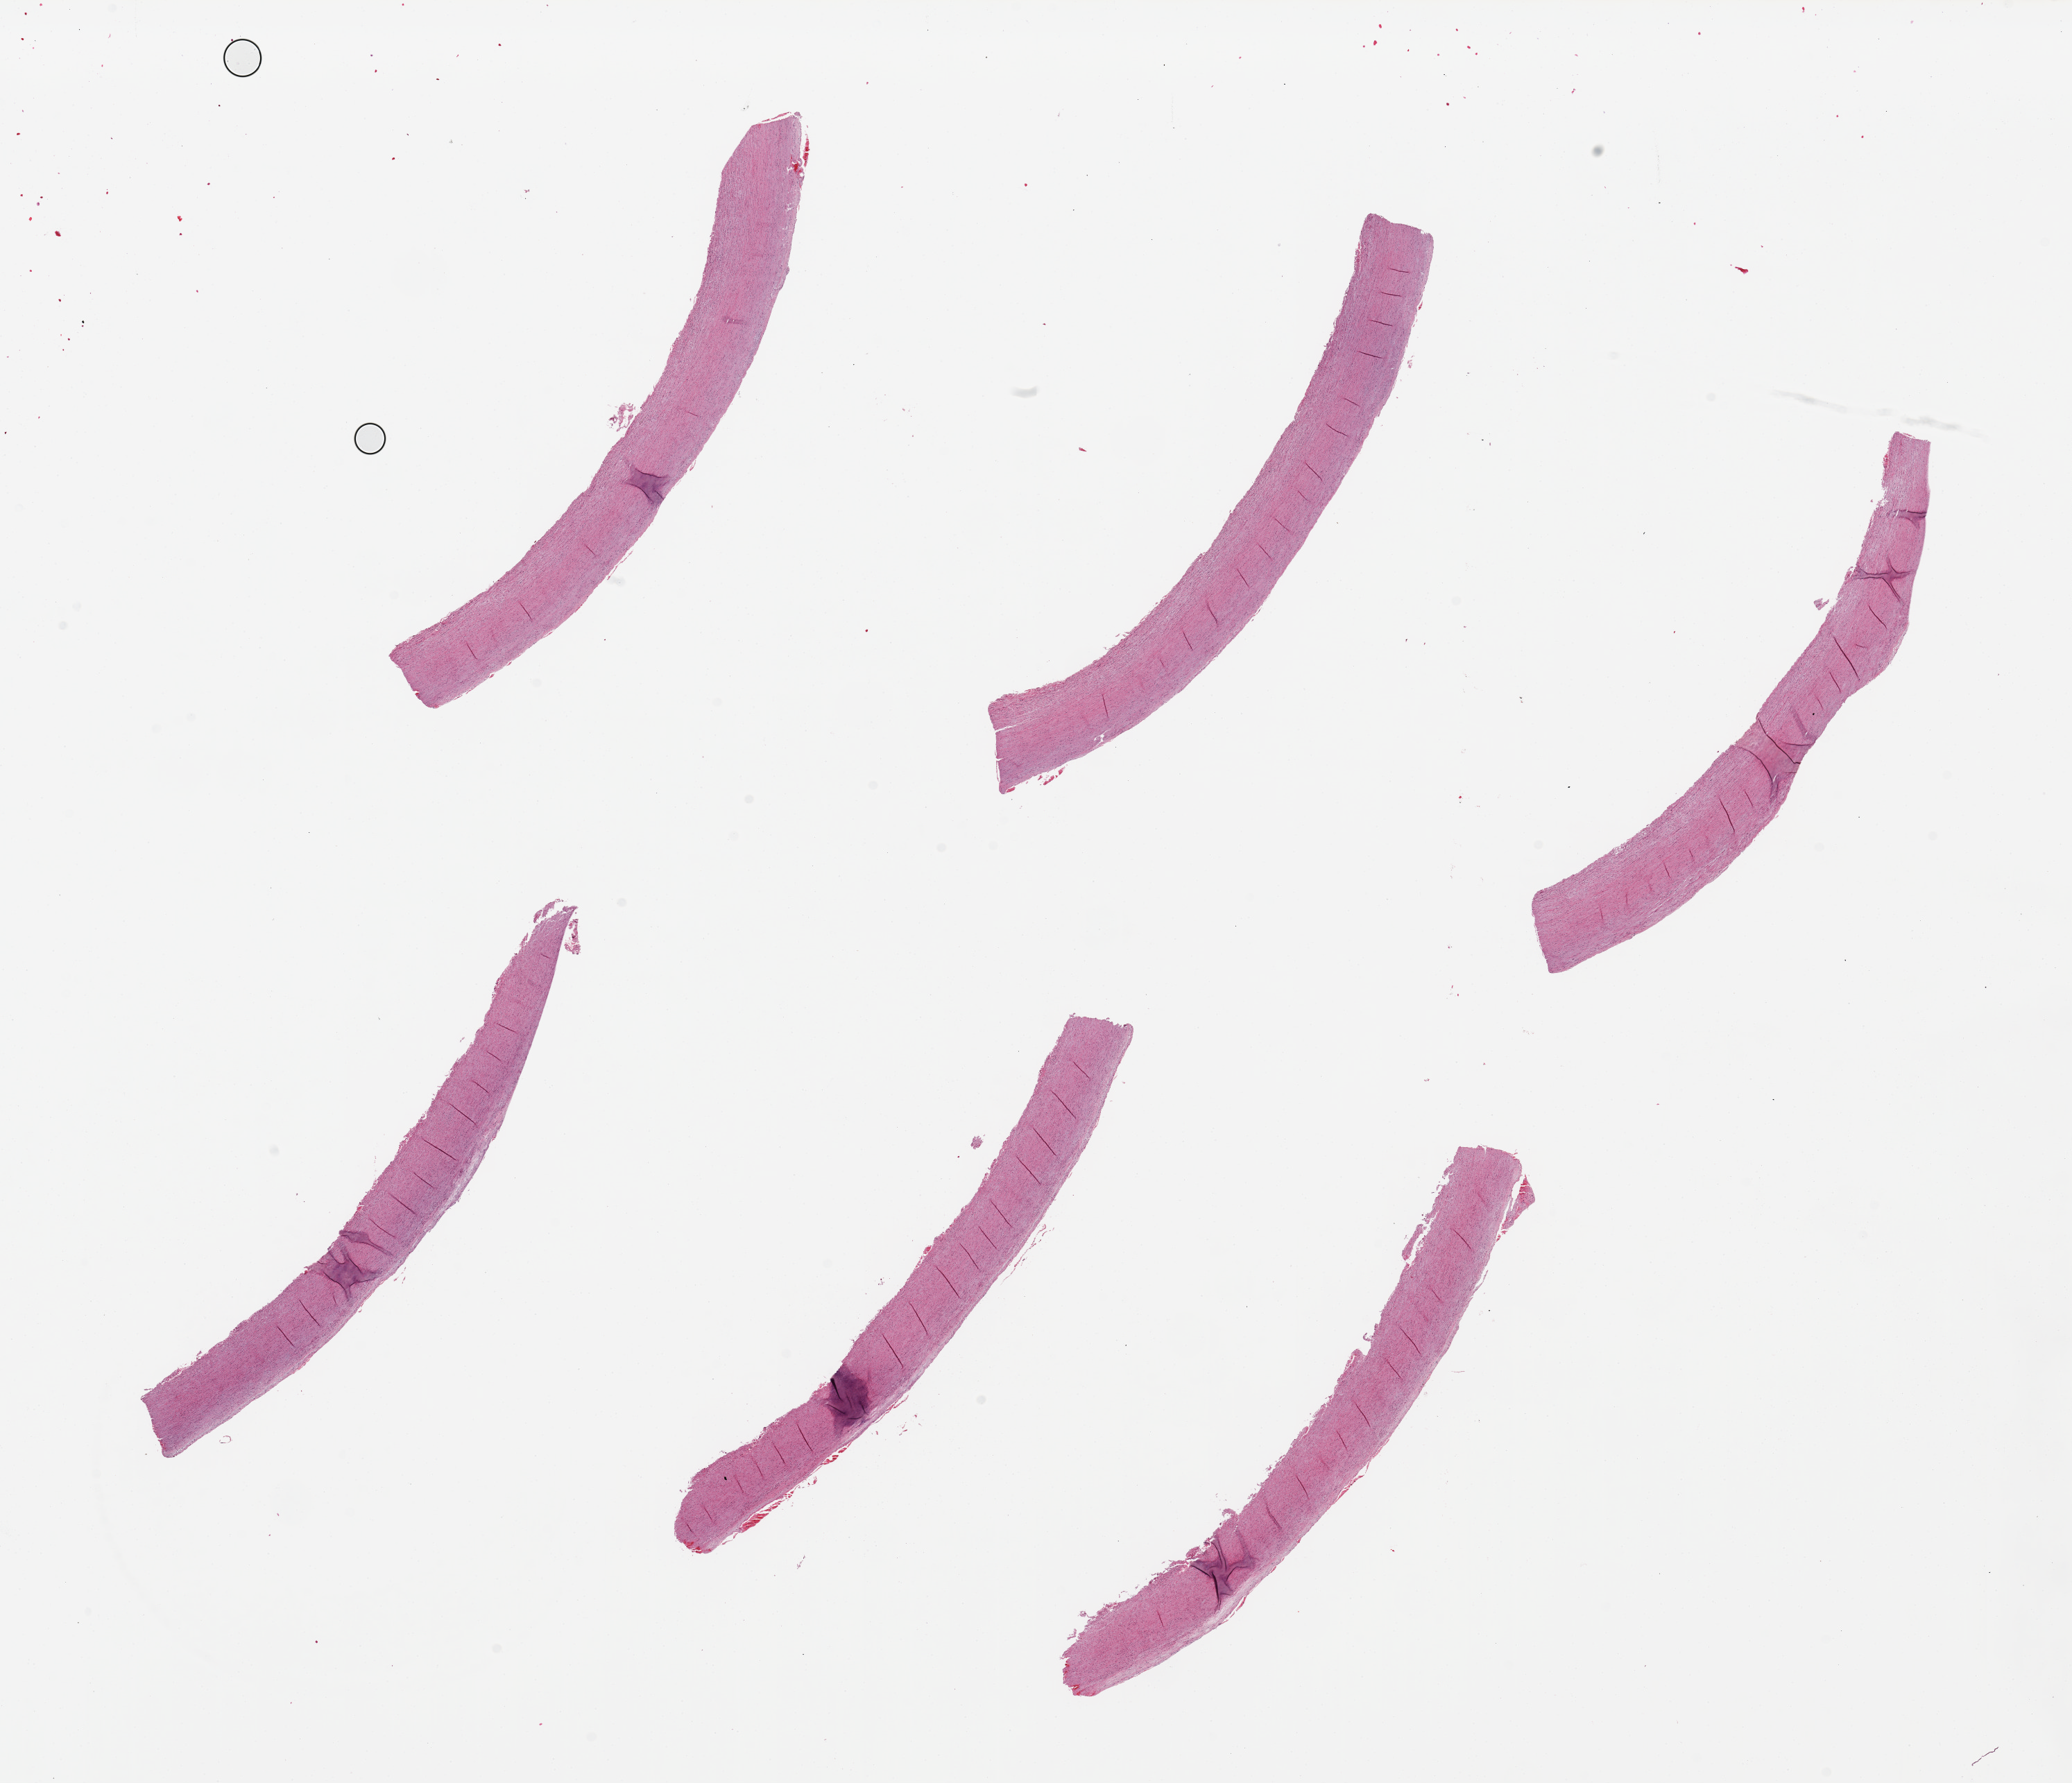
Hematoxylin and eosin (H&E) whole-slide image — shown as a low-resolution overview of the whole scanned area (about 23.6 x 20.3 mm, acquisition: 20x scan), PAXgene-fixed, paraffin-embedded tissue, target tissue: aorta, donor tissue sample. Donor sex: male.
Review note (as recorded): 6 pieces up to 8x1mm.